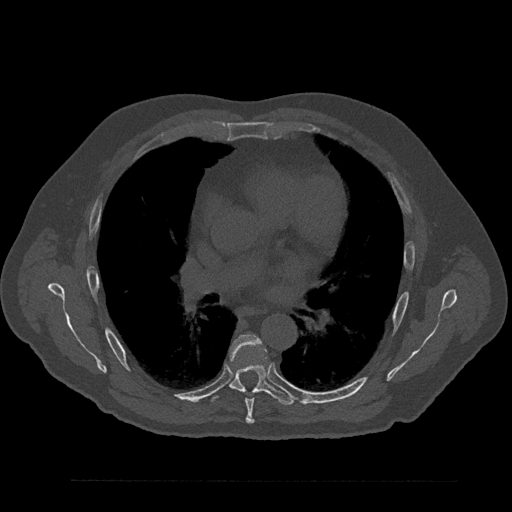
CT including the spine, one axial slice. Slice 529 of 797 in the series (ordered by position). Reconstruction kernel Br40s/3. 120 kVp. Bone window (W 1800 / L 400 HU). 0.5 mm slice thickness. 512 × 512 image matrix, field of view 430 × 430 mm. Male patient, age 61 years. Case-level facts recorded for this patient, not image findings: primary cancer: prostate.
Outlined on this slice (semi-automatically segmented with operator editing):
- T6 vertebra: bounding box <230,335,266,424> (left, top, right, bottom; pixels)
- T7 vertebra: <210,350,294,406>